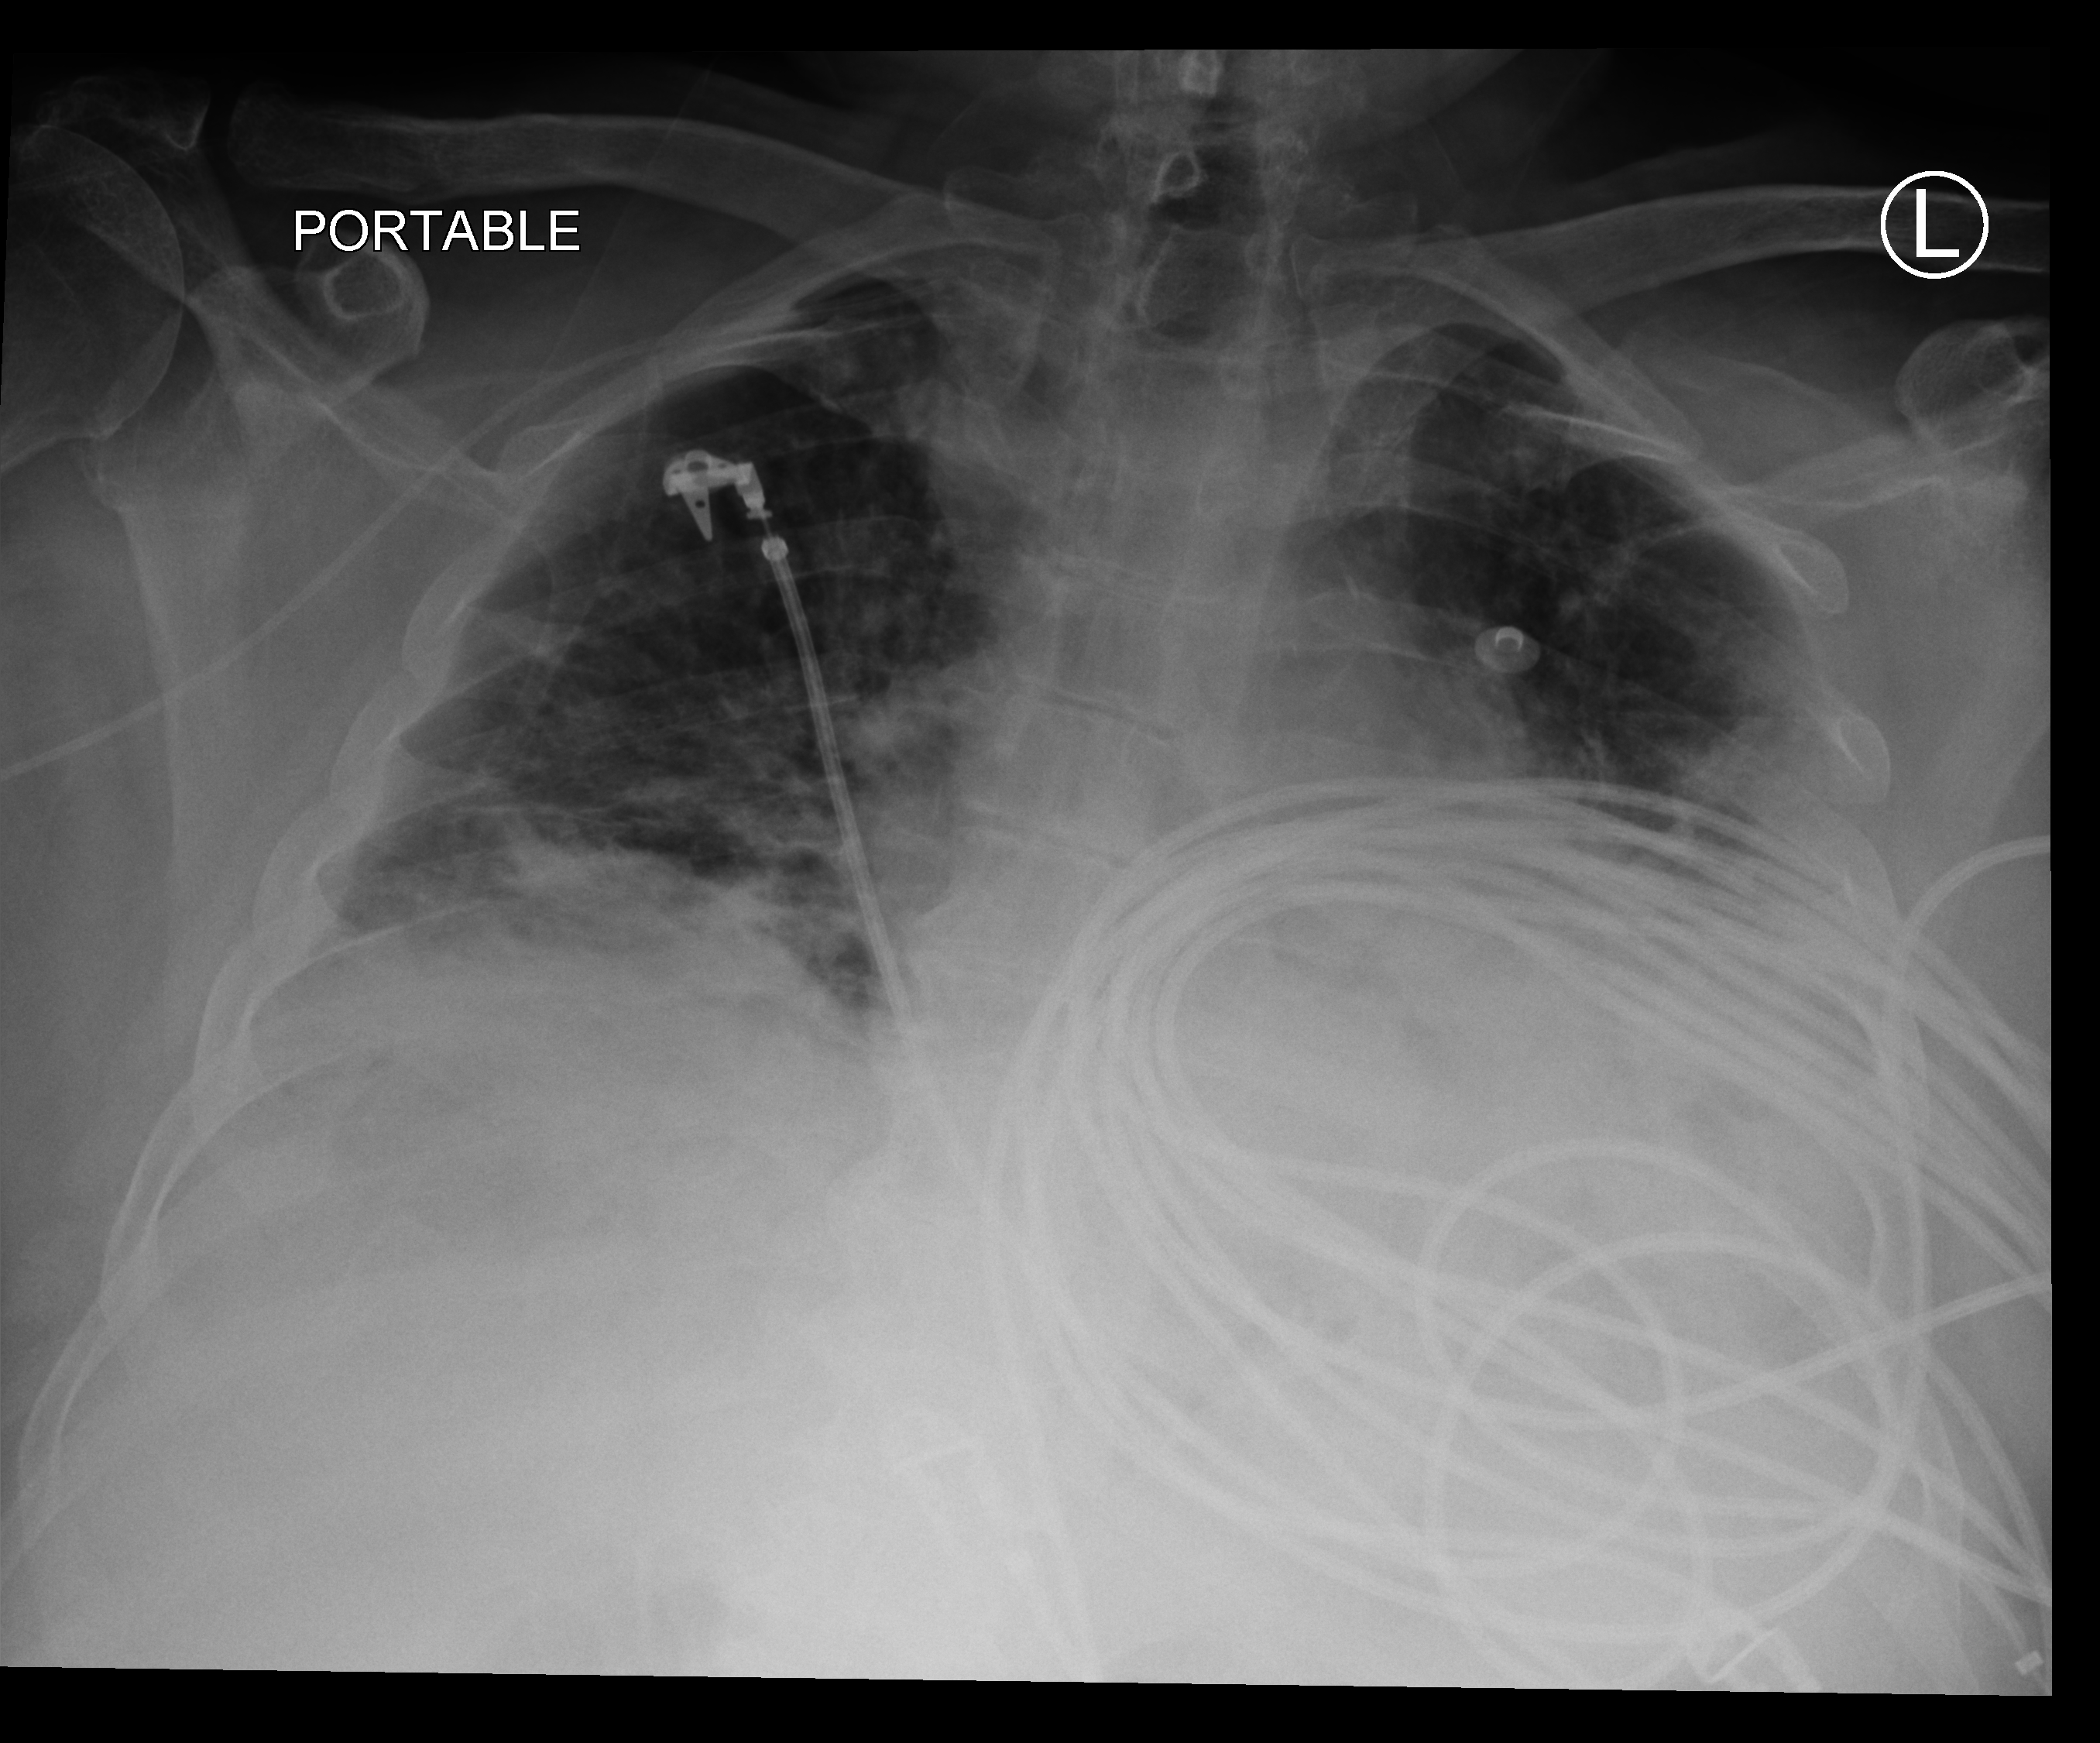
Chest X-ray (portable), anteroposterior (AP) projection. Male patient hospitalised with COVID-19, age 60–74 years.
Admission-level facts for this patient (not findings on this image; timing relative to this image not recorded): smoking status (admission record): never; mechanically ventilated during this hospital stay: yes.